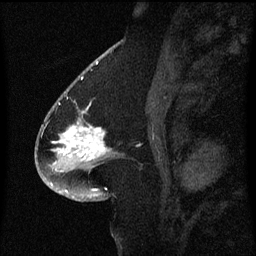
Breast MRI (dynamic contrast-enhanced), one sagittal slice. Slice 30 of 60 in the series (ordered by position). Dynamic contrast-enhanced series, image 2 of 3 at this slice position (ordered by acquisition). 1.5 T. TE 4.2 ms, TR 8.4 ms. 256 × 256 image matrix, field of view 200 × 200 mm. Female patient, age 54 years. Case-level facts recorded for this patient, not image findings: setting: breast cancer imaged before/during neoadjuvant chemotherapy; receptor status: HR-positive, HER2-negative.
Outlined on this slice (semi-automatically segmented with operator editing):
- analysis volume of interest (the breast-tissue region the enhancement analysis was run in; not a lesion): bounding box <46,100,115,171> (left, top, right, bottom; pixels)
- tumour enhancement mask (voxels above the 70 % enhancement threshold inside the analysis volume of interest): <55,126,106,151>